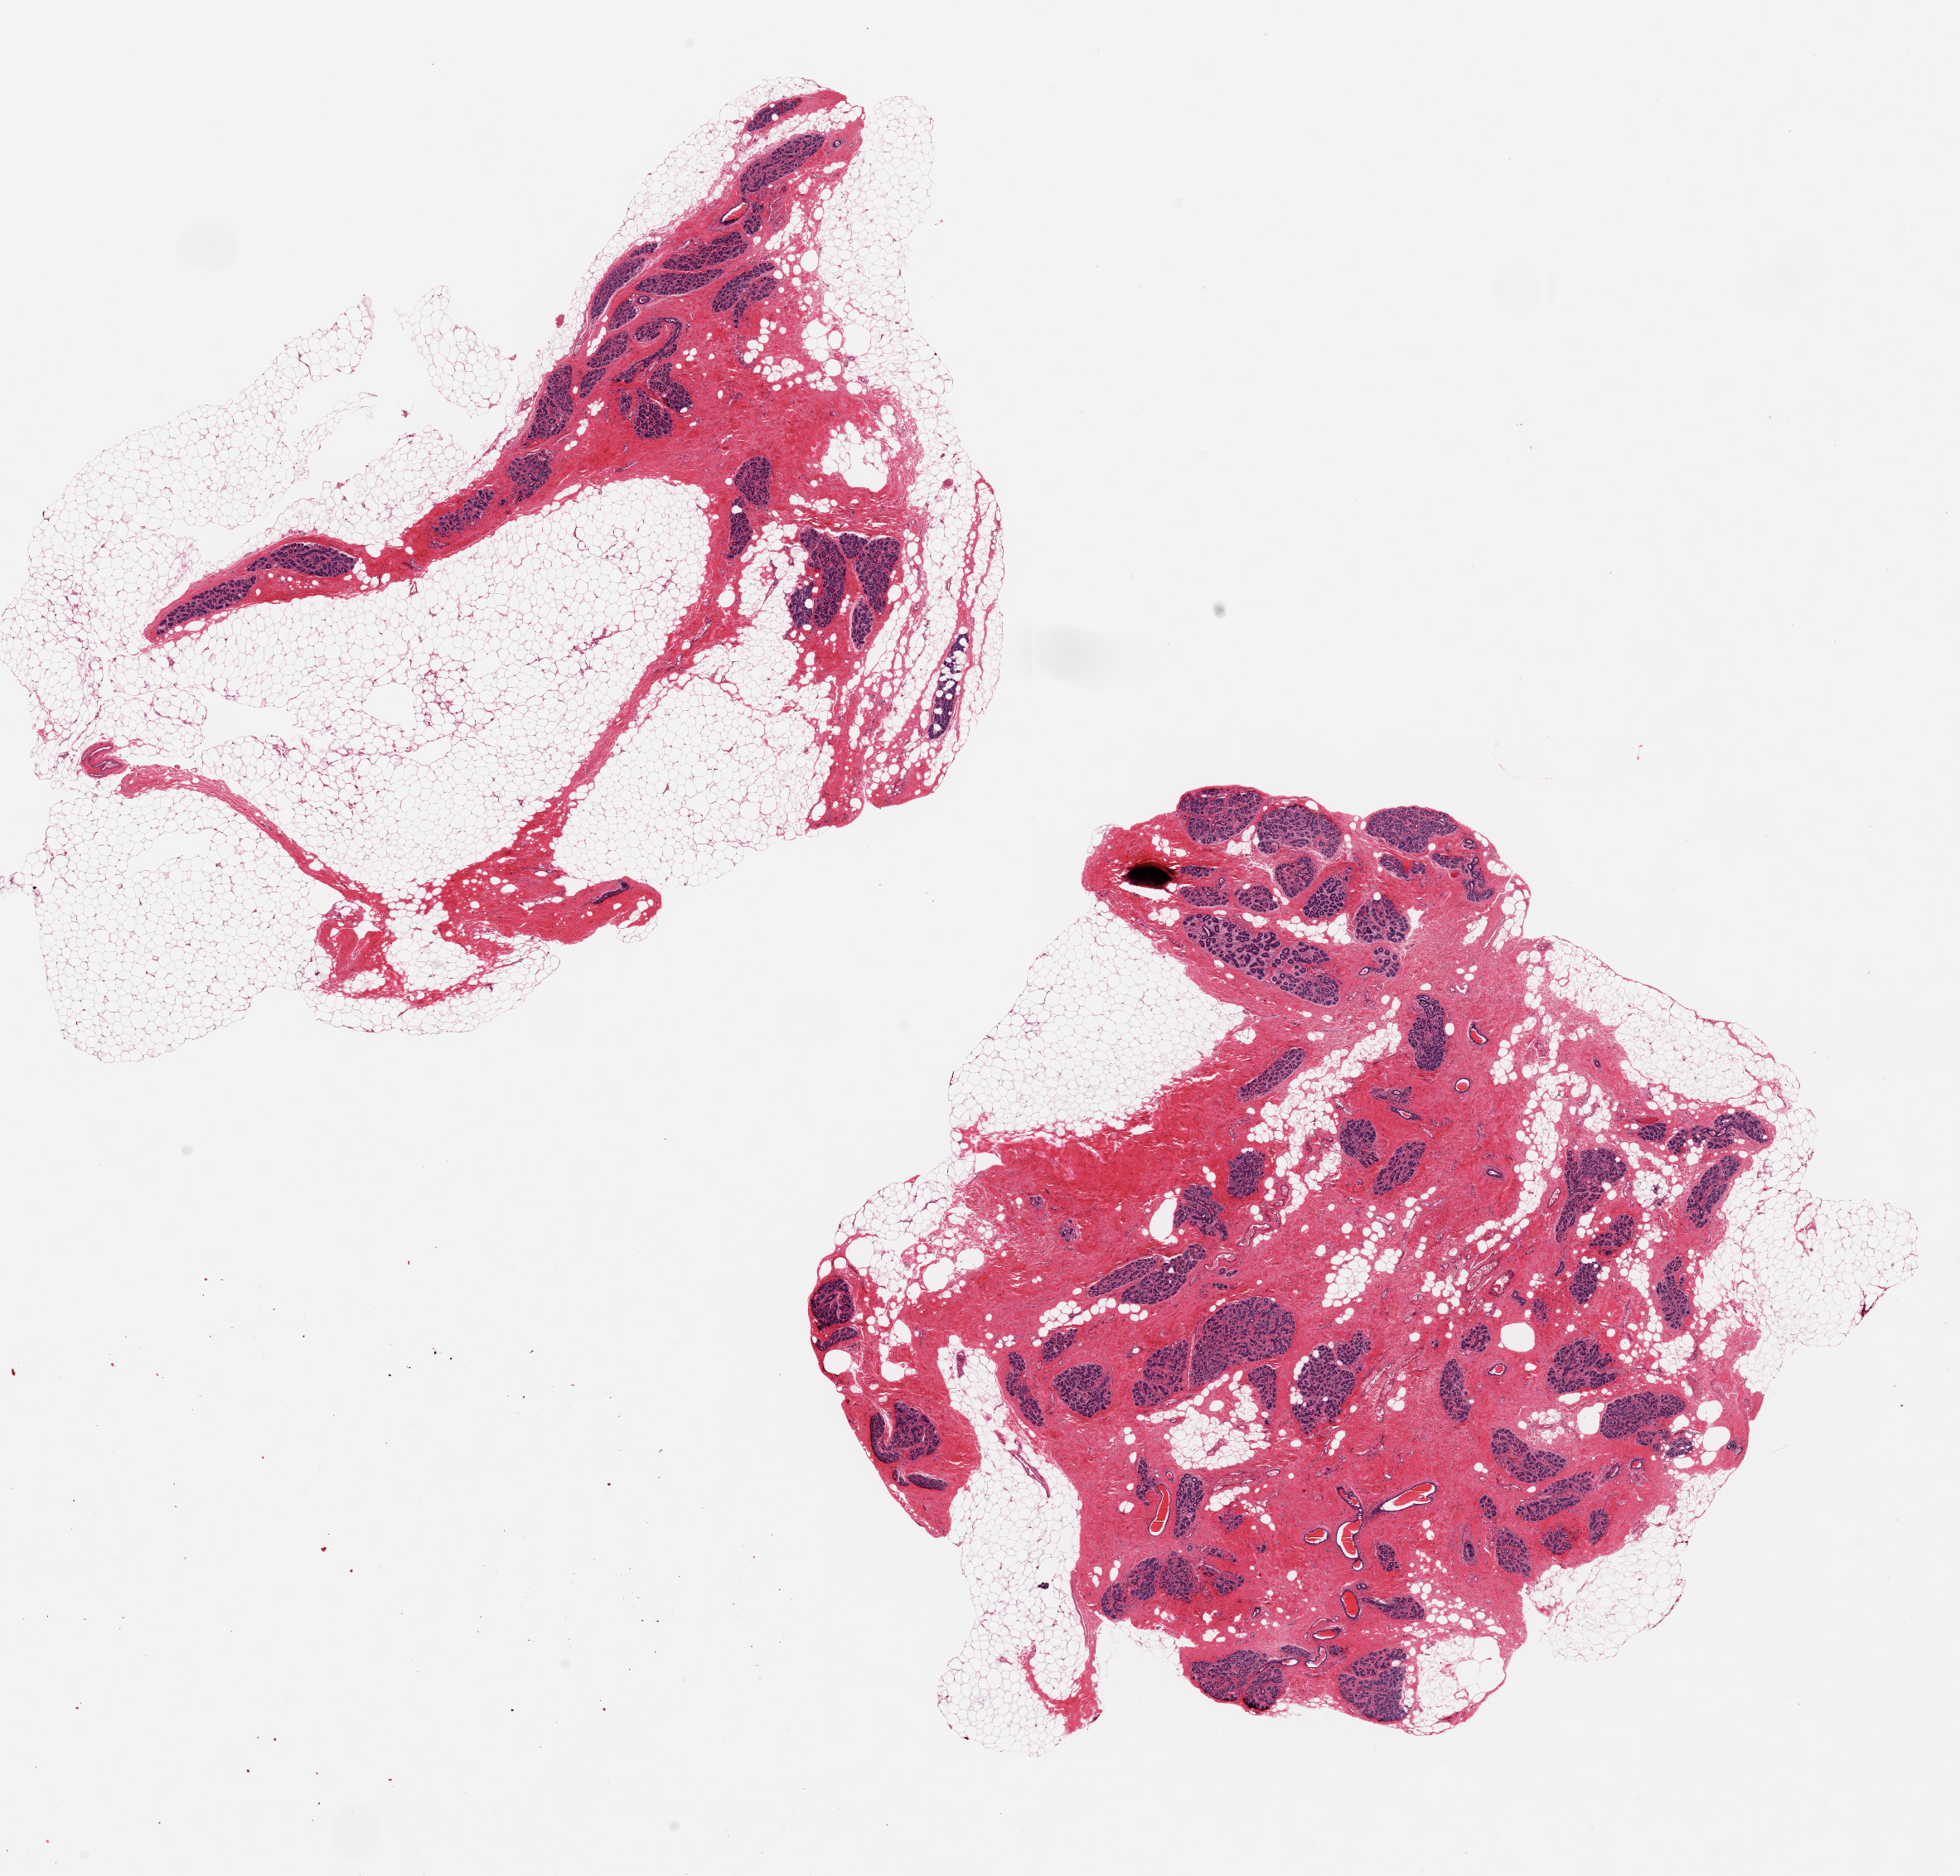
Whole-slide image, H&E stain, brightfield, shown as a low-resolution overview of the whole scanned area (about 18.7 x 17.9 mm); PAXgene-fixed, paraffin-embedded tissue; section of breast (target tissue); donor tissue sample. Donor: female.
Review note (as recorded): 2 ~9x7mm aliquots, ~ 70% ductal/lobular units, good specimen.